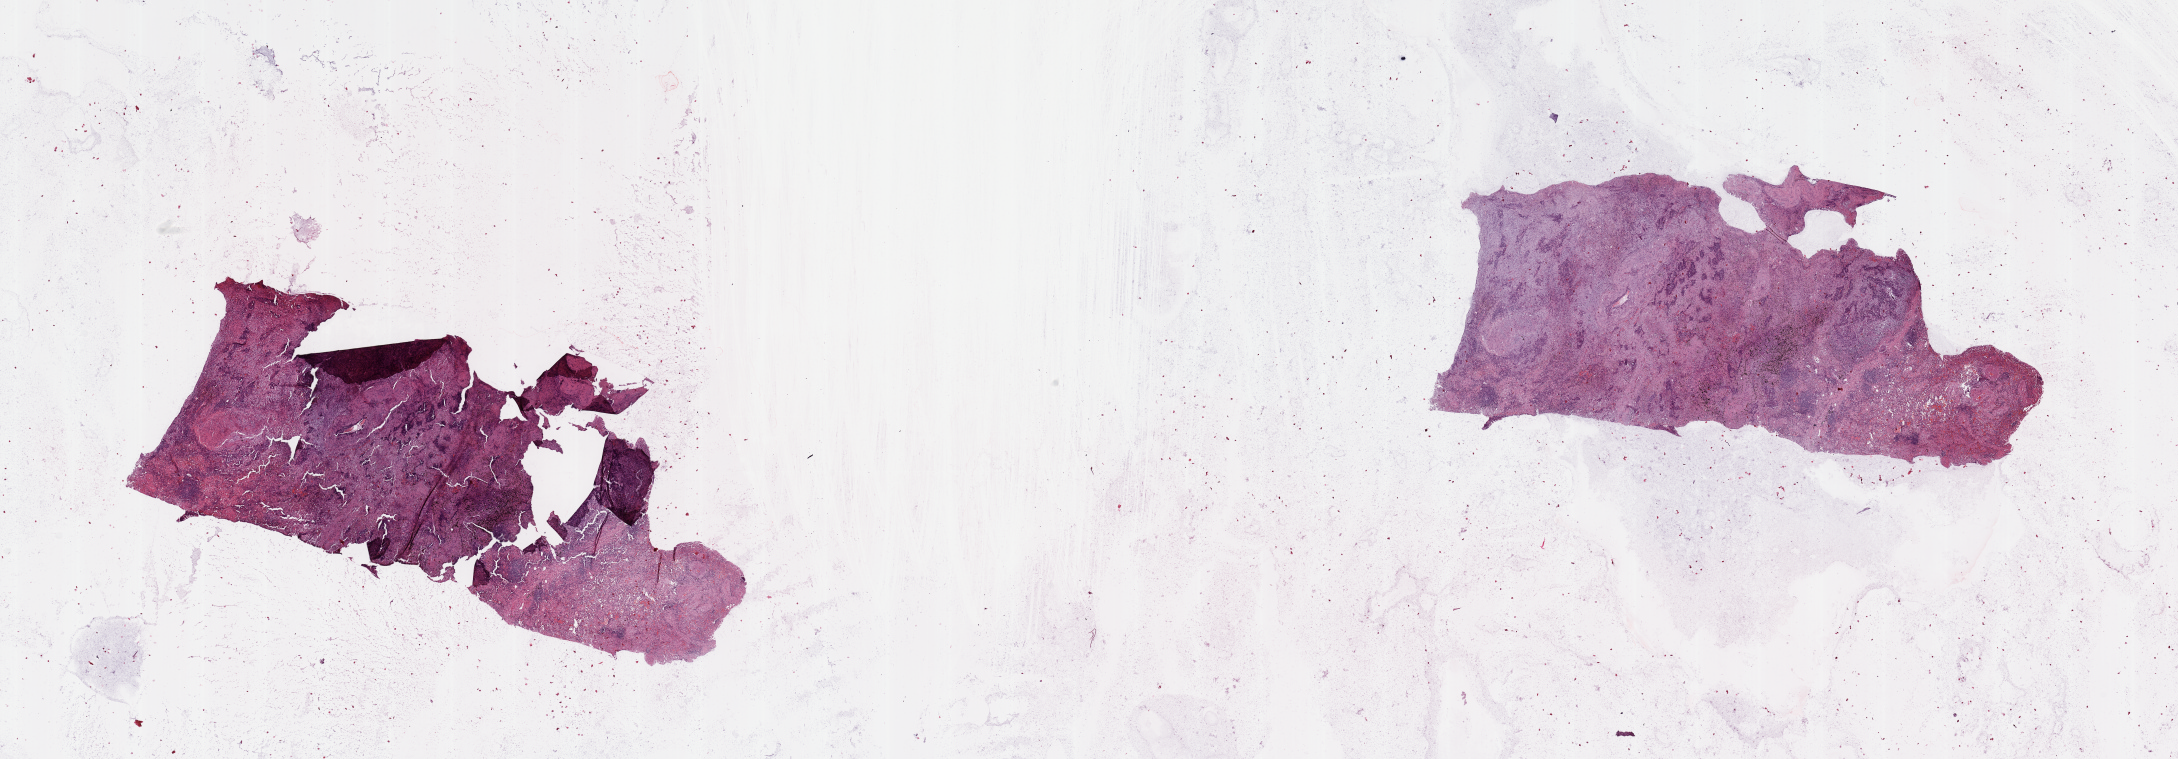
Whole-slide histology image, H&E, low-resolution overview of the scanned area, about 34.5 x 12.0 mm. Tumour tissue sample, lung. Male, 72 y/o. Histologic grade: G3 (poorly differentiated).
- AJCC pathologic stage: IIIA
- diagnosis: Squamous cell carcinoma, NOS